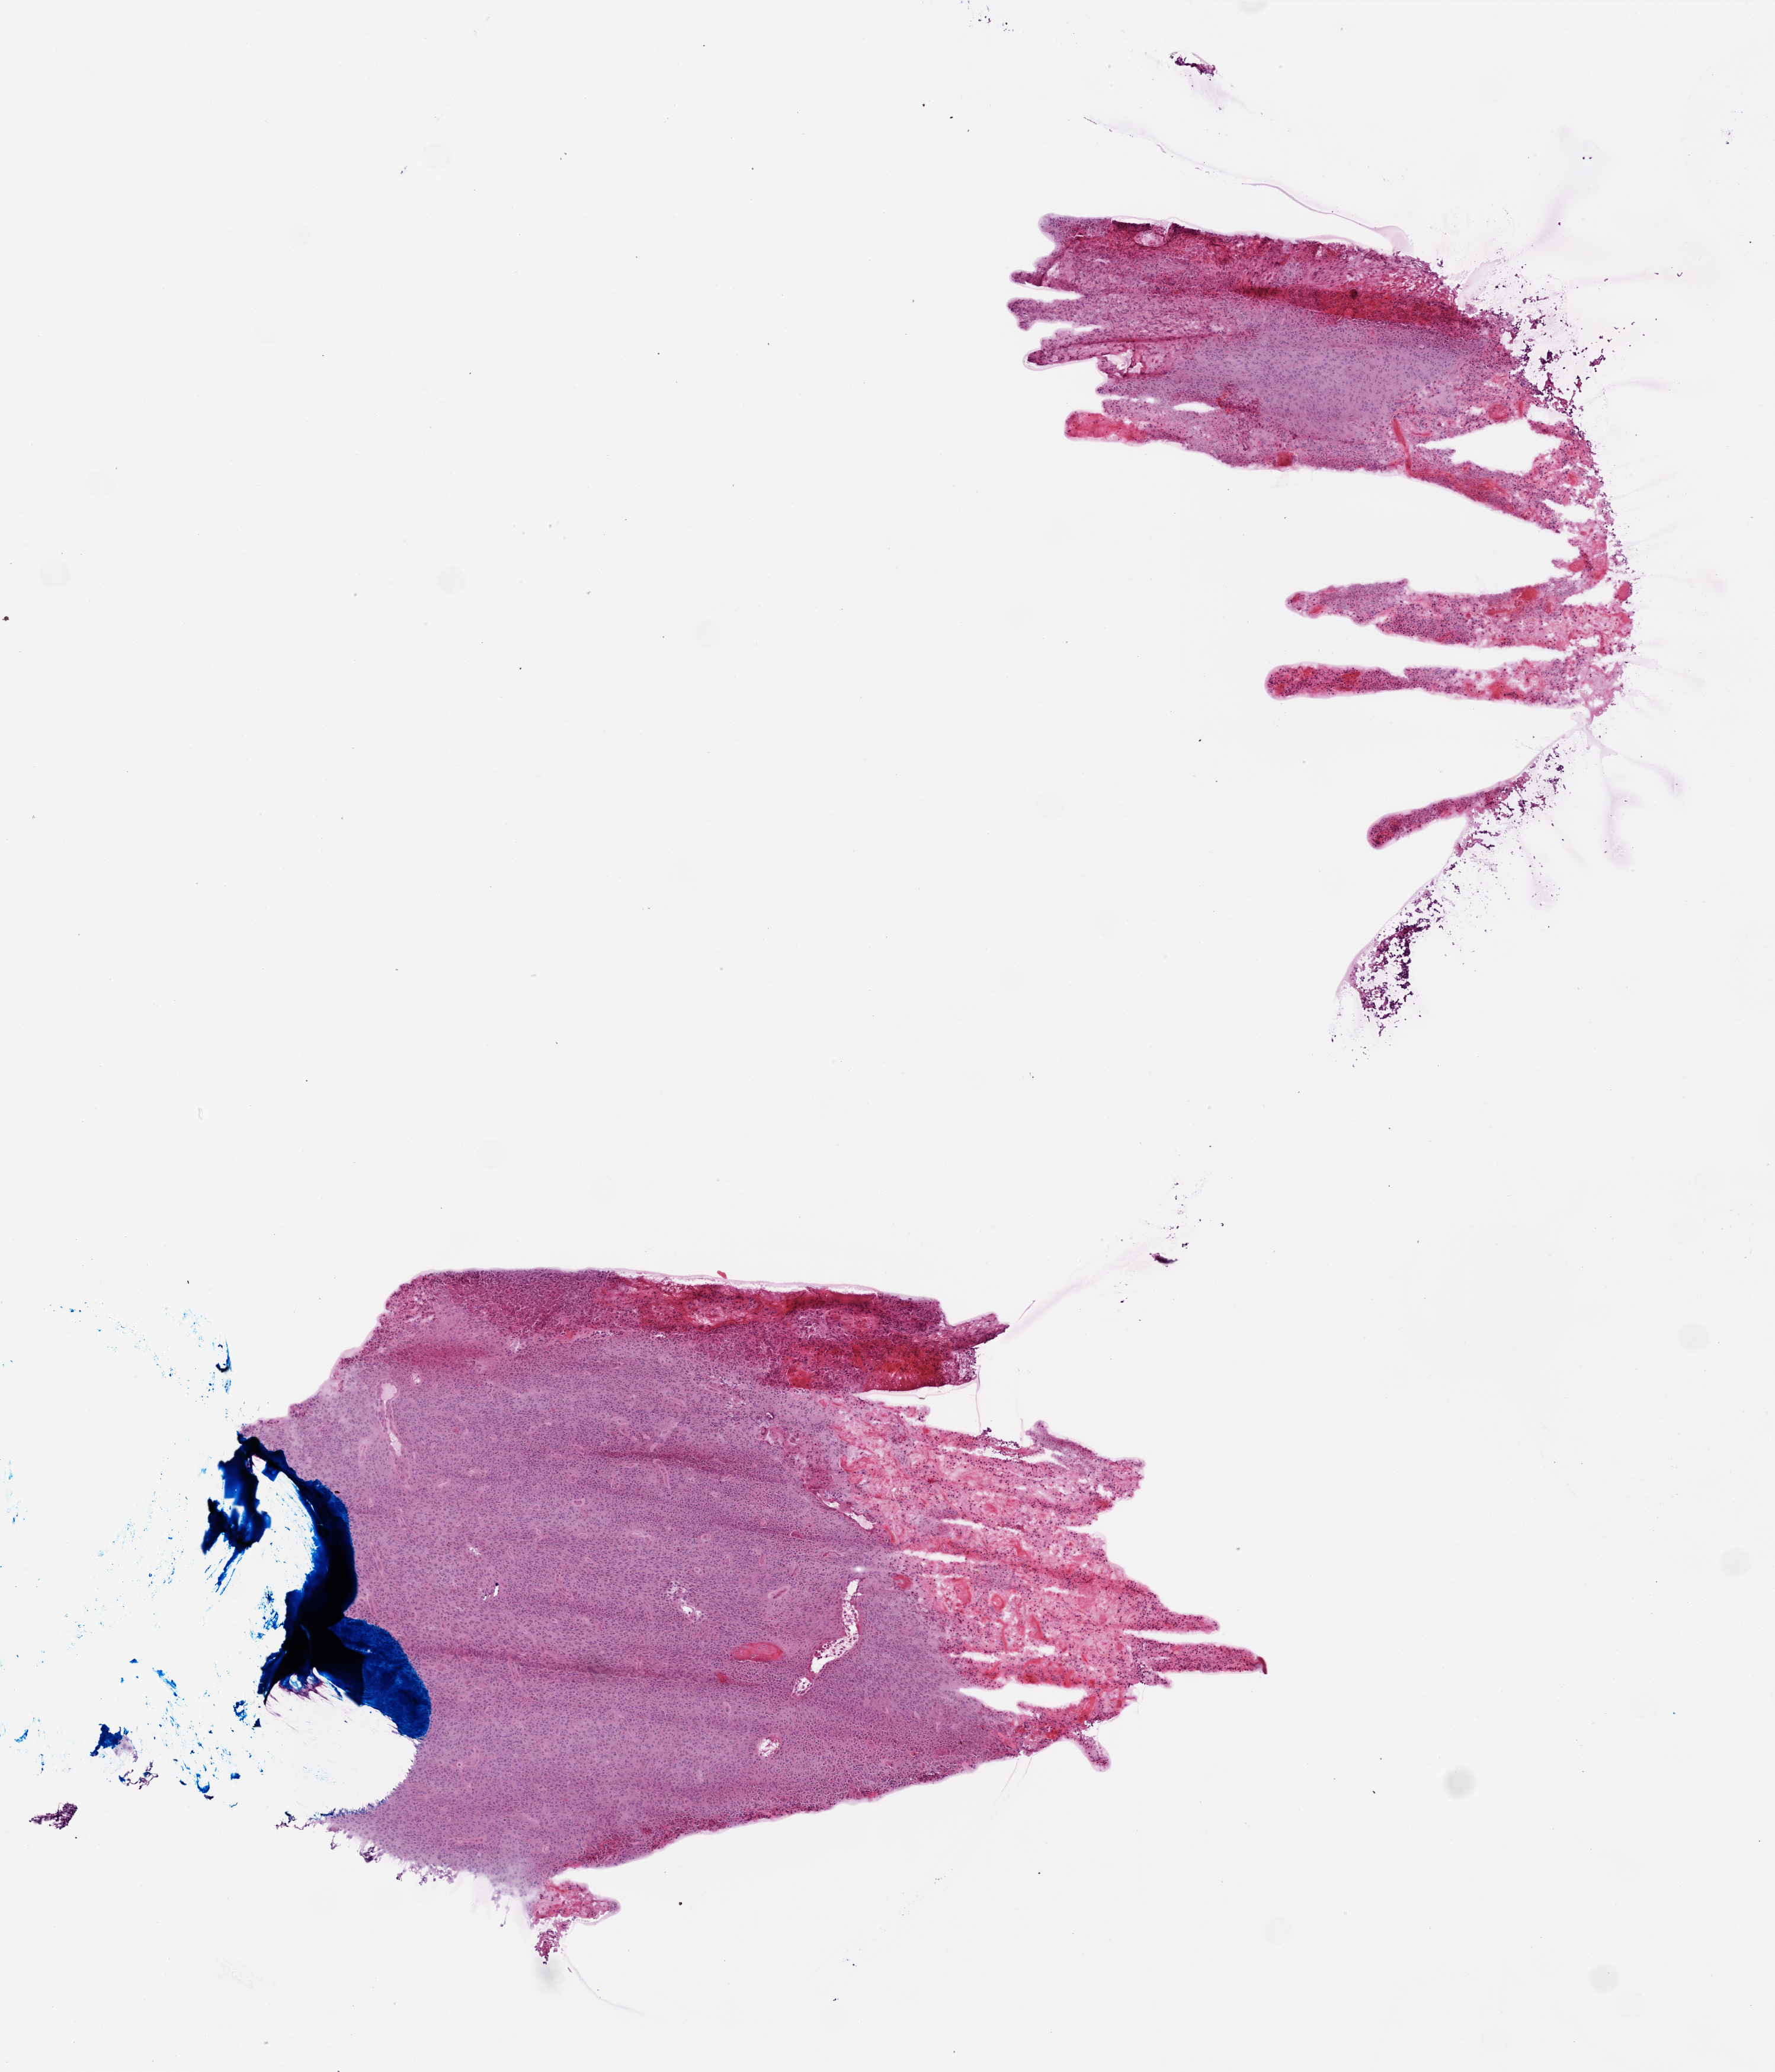
Hematoxylin and eosin (H&E) stained whole-slide image — a low-resolution overview of the entire scanned area, about 6.0 x 7.0 mm; frozen section from the top of the tissue portion; brain, primary tumour sample. Patient: female, age at initial diagnosis 51 years. Slide review estimates, as recorded: tumour cells 80%, tumour nuclei 100%, normal cells 0%, stromal cells 0%, necrosis 20%.
* histologic diagnosis: Glioblastoma